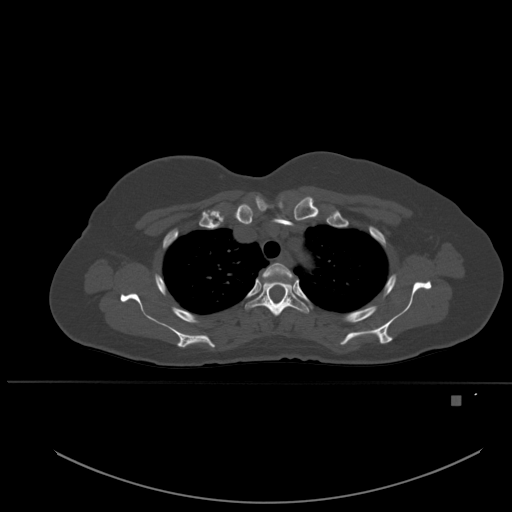
CT including the spine, one axial slice. Slice 396 of 651 in the series (ordered by position). Bone window (W 1800 / L 400 HU). 1.5 mm slice thickness. 512 × 512 image matrix. Female patient, age 49 years. From the clinical record (not read from this slice): primary cancer: breast; vertebrae with lytic lesions (as recorded): L3, T12, L4.
Annotated regions visible in this slice (semi-automatic segmentation, software-assisted and operator-edited):
- T2 vertebra: bounding box [x1, y1, x2, y2] px = [262, 263, 296, 281]
- T3 vertebra: [246, 279, 309, 317]